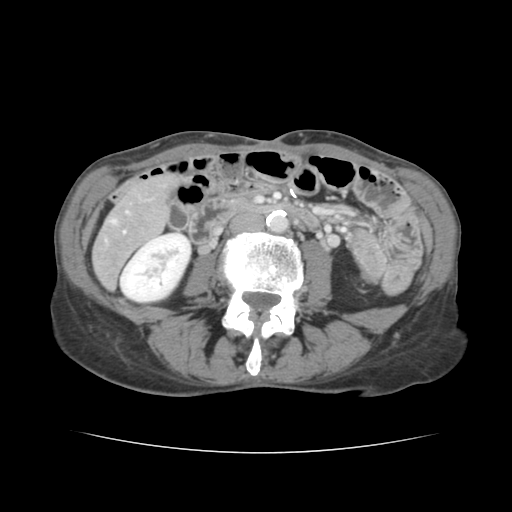
Contrast-enhanced abdominal CT, one axial slice. Position 32 of 136 along the scan axis. Intravenous contrast given. Soft-tissue window (W 400 / L 40 HU). 512 × 512 image matrix. Female patient, age 77 years. From the clinical record (not read from this slice): diagnosis: colorectal cancer liver metastases, imaged before liver resection; multiple liver metastases: yes; largest metastasis: 3 cm; disease in both lobes: no.
Annotated regions visible in this slice (expert manual segmentation):
- hepatic veins: bounding box (x1, y1, x2, y2) in pixels: (111, 221, 114, 223)
- liver: (94, 176, 175, 287)
- portal vein (with intrahepatic branches): (123, 231, 125, 233)